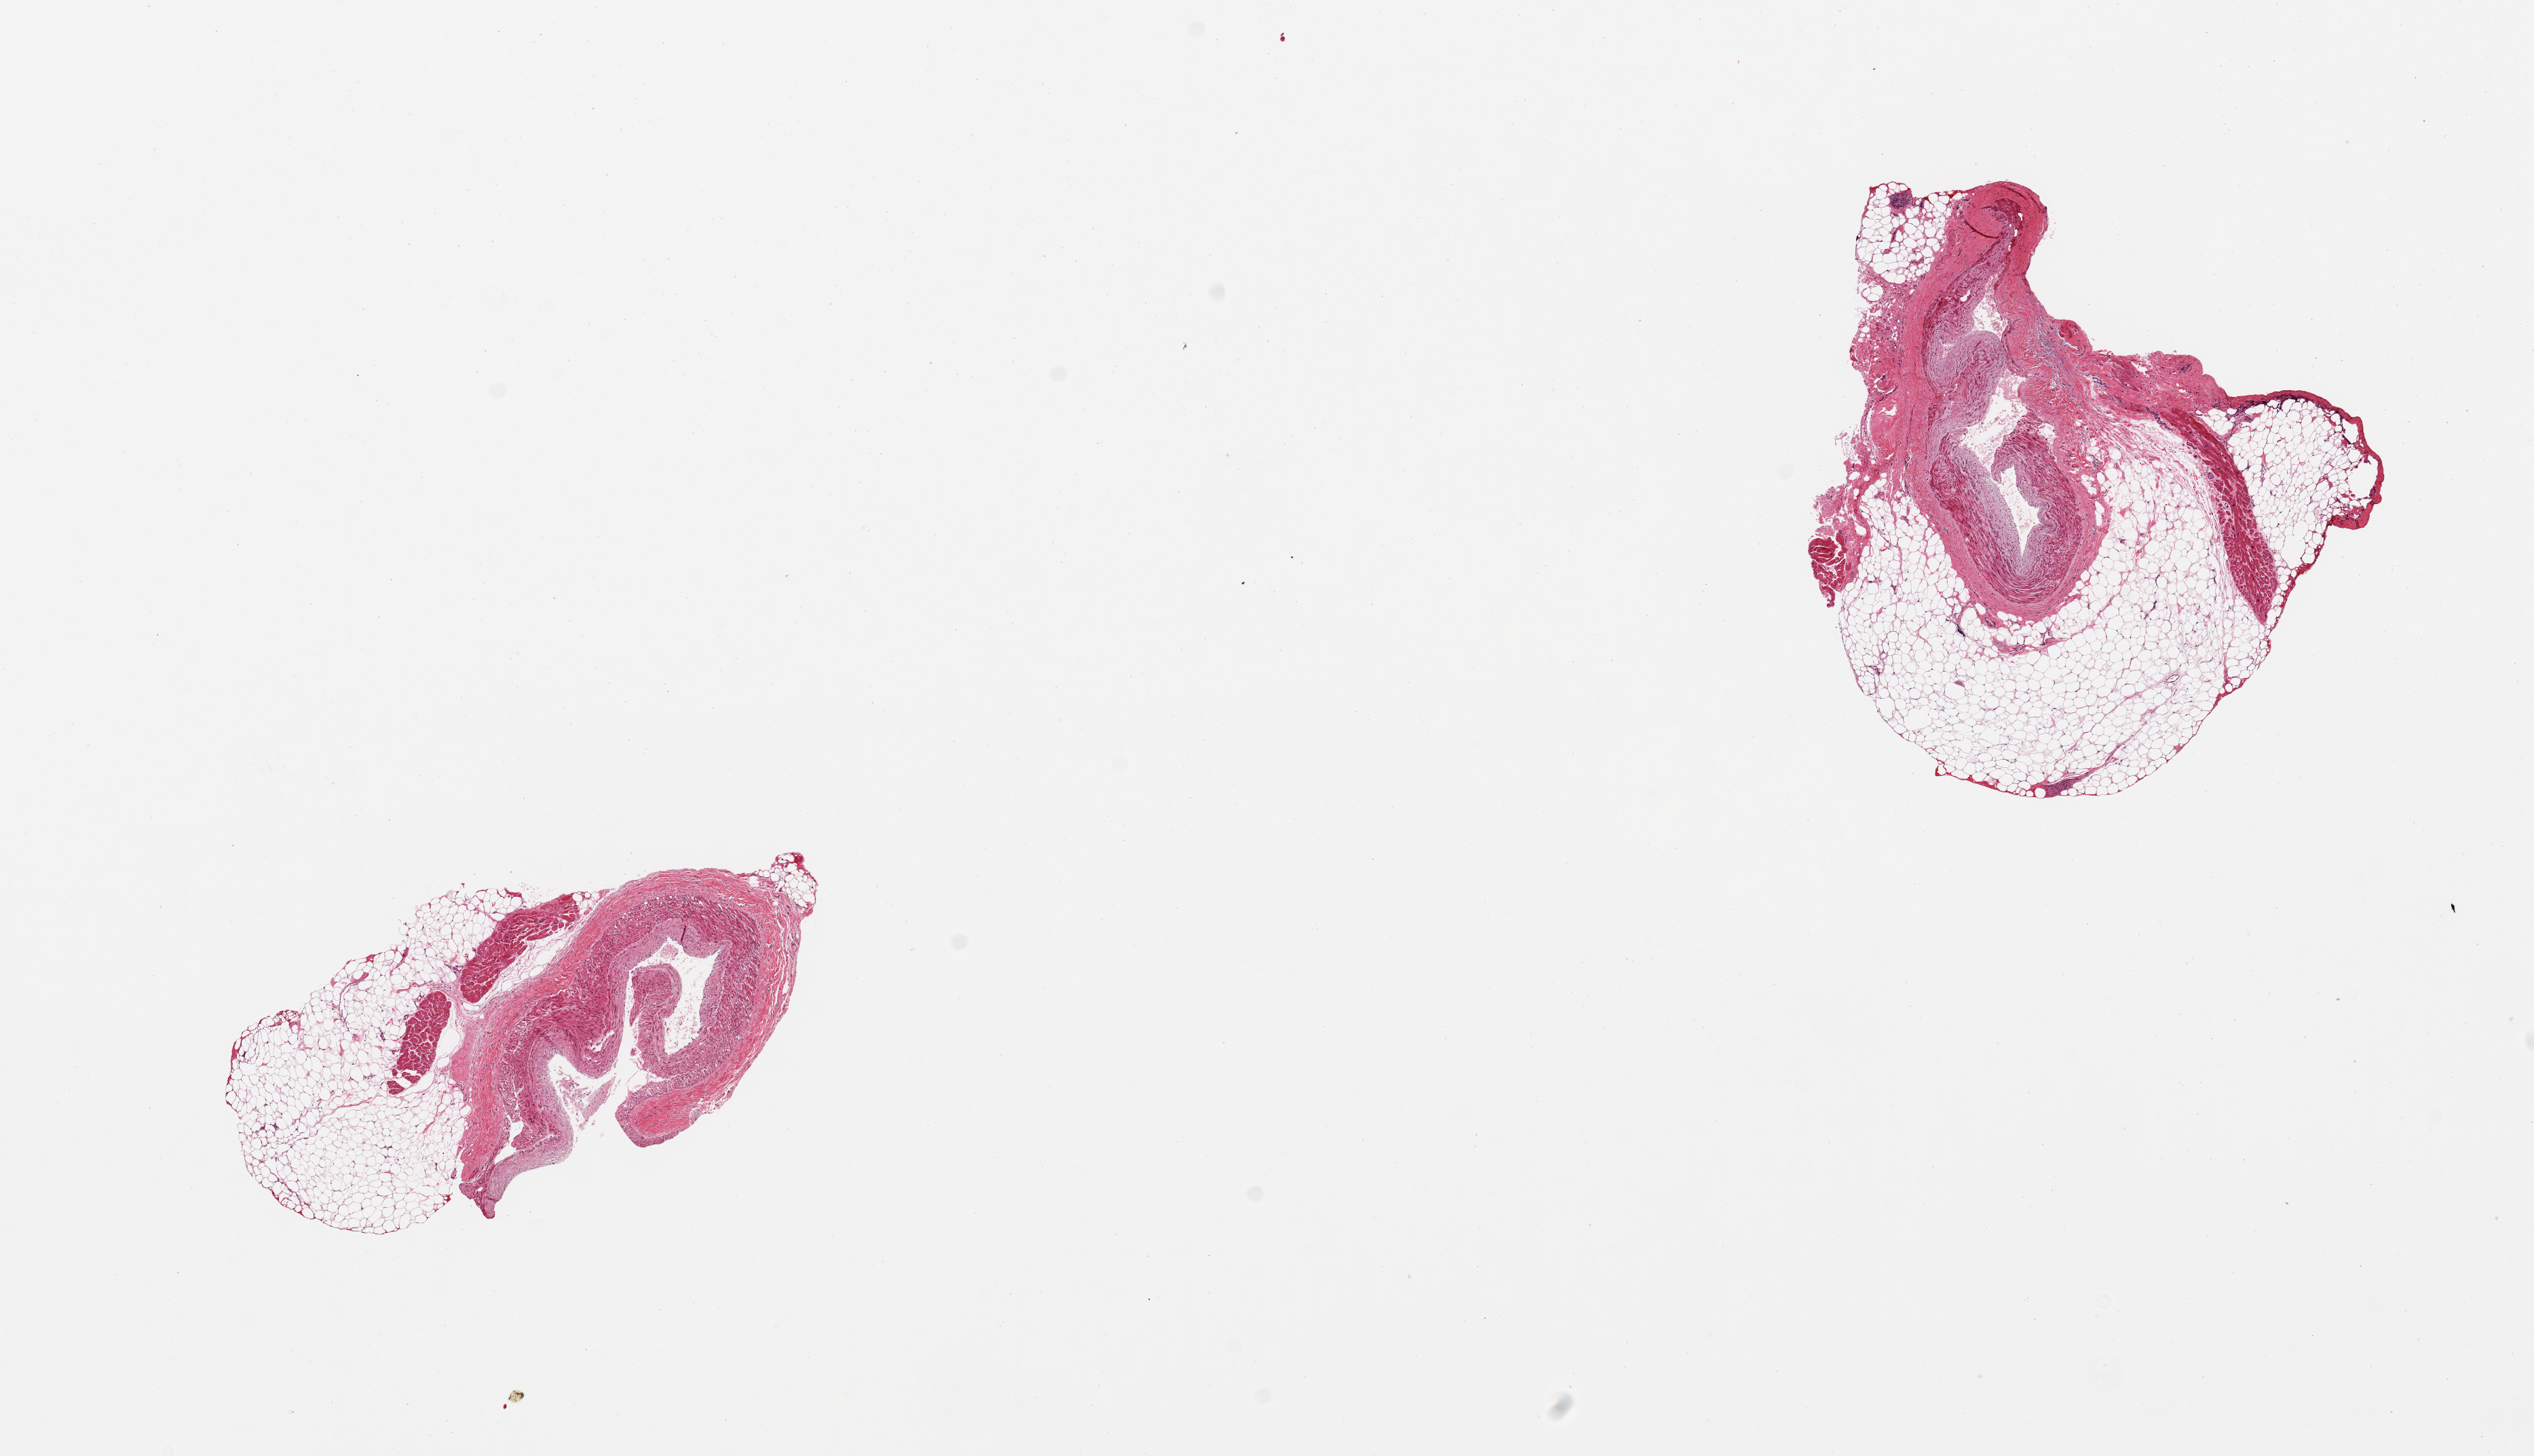
Digitized H&E-stained section, brightfield, a low-resolution overview of the entire scanned area, about 14.8 x 8.5 mm; PAXgene-fixed paraffin-embedded (PFPE) section; sampled site (target tissue): coronary artery; tissue donor sample. Male donor.
Reviewer comment on this tissue sample: 2 pieces; poorly trimmed: both pieces have at least 50% extraneous fat and myocardium.